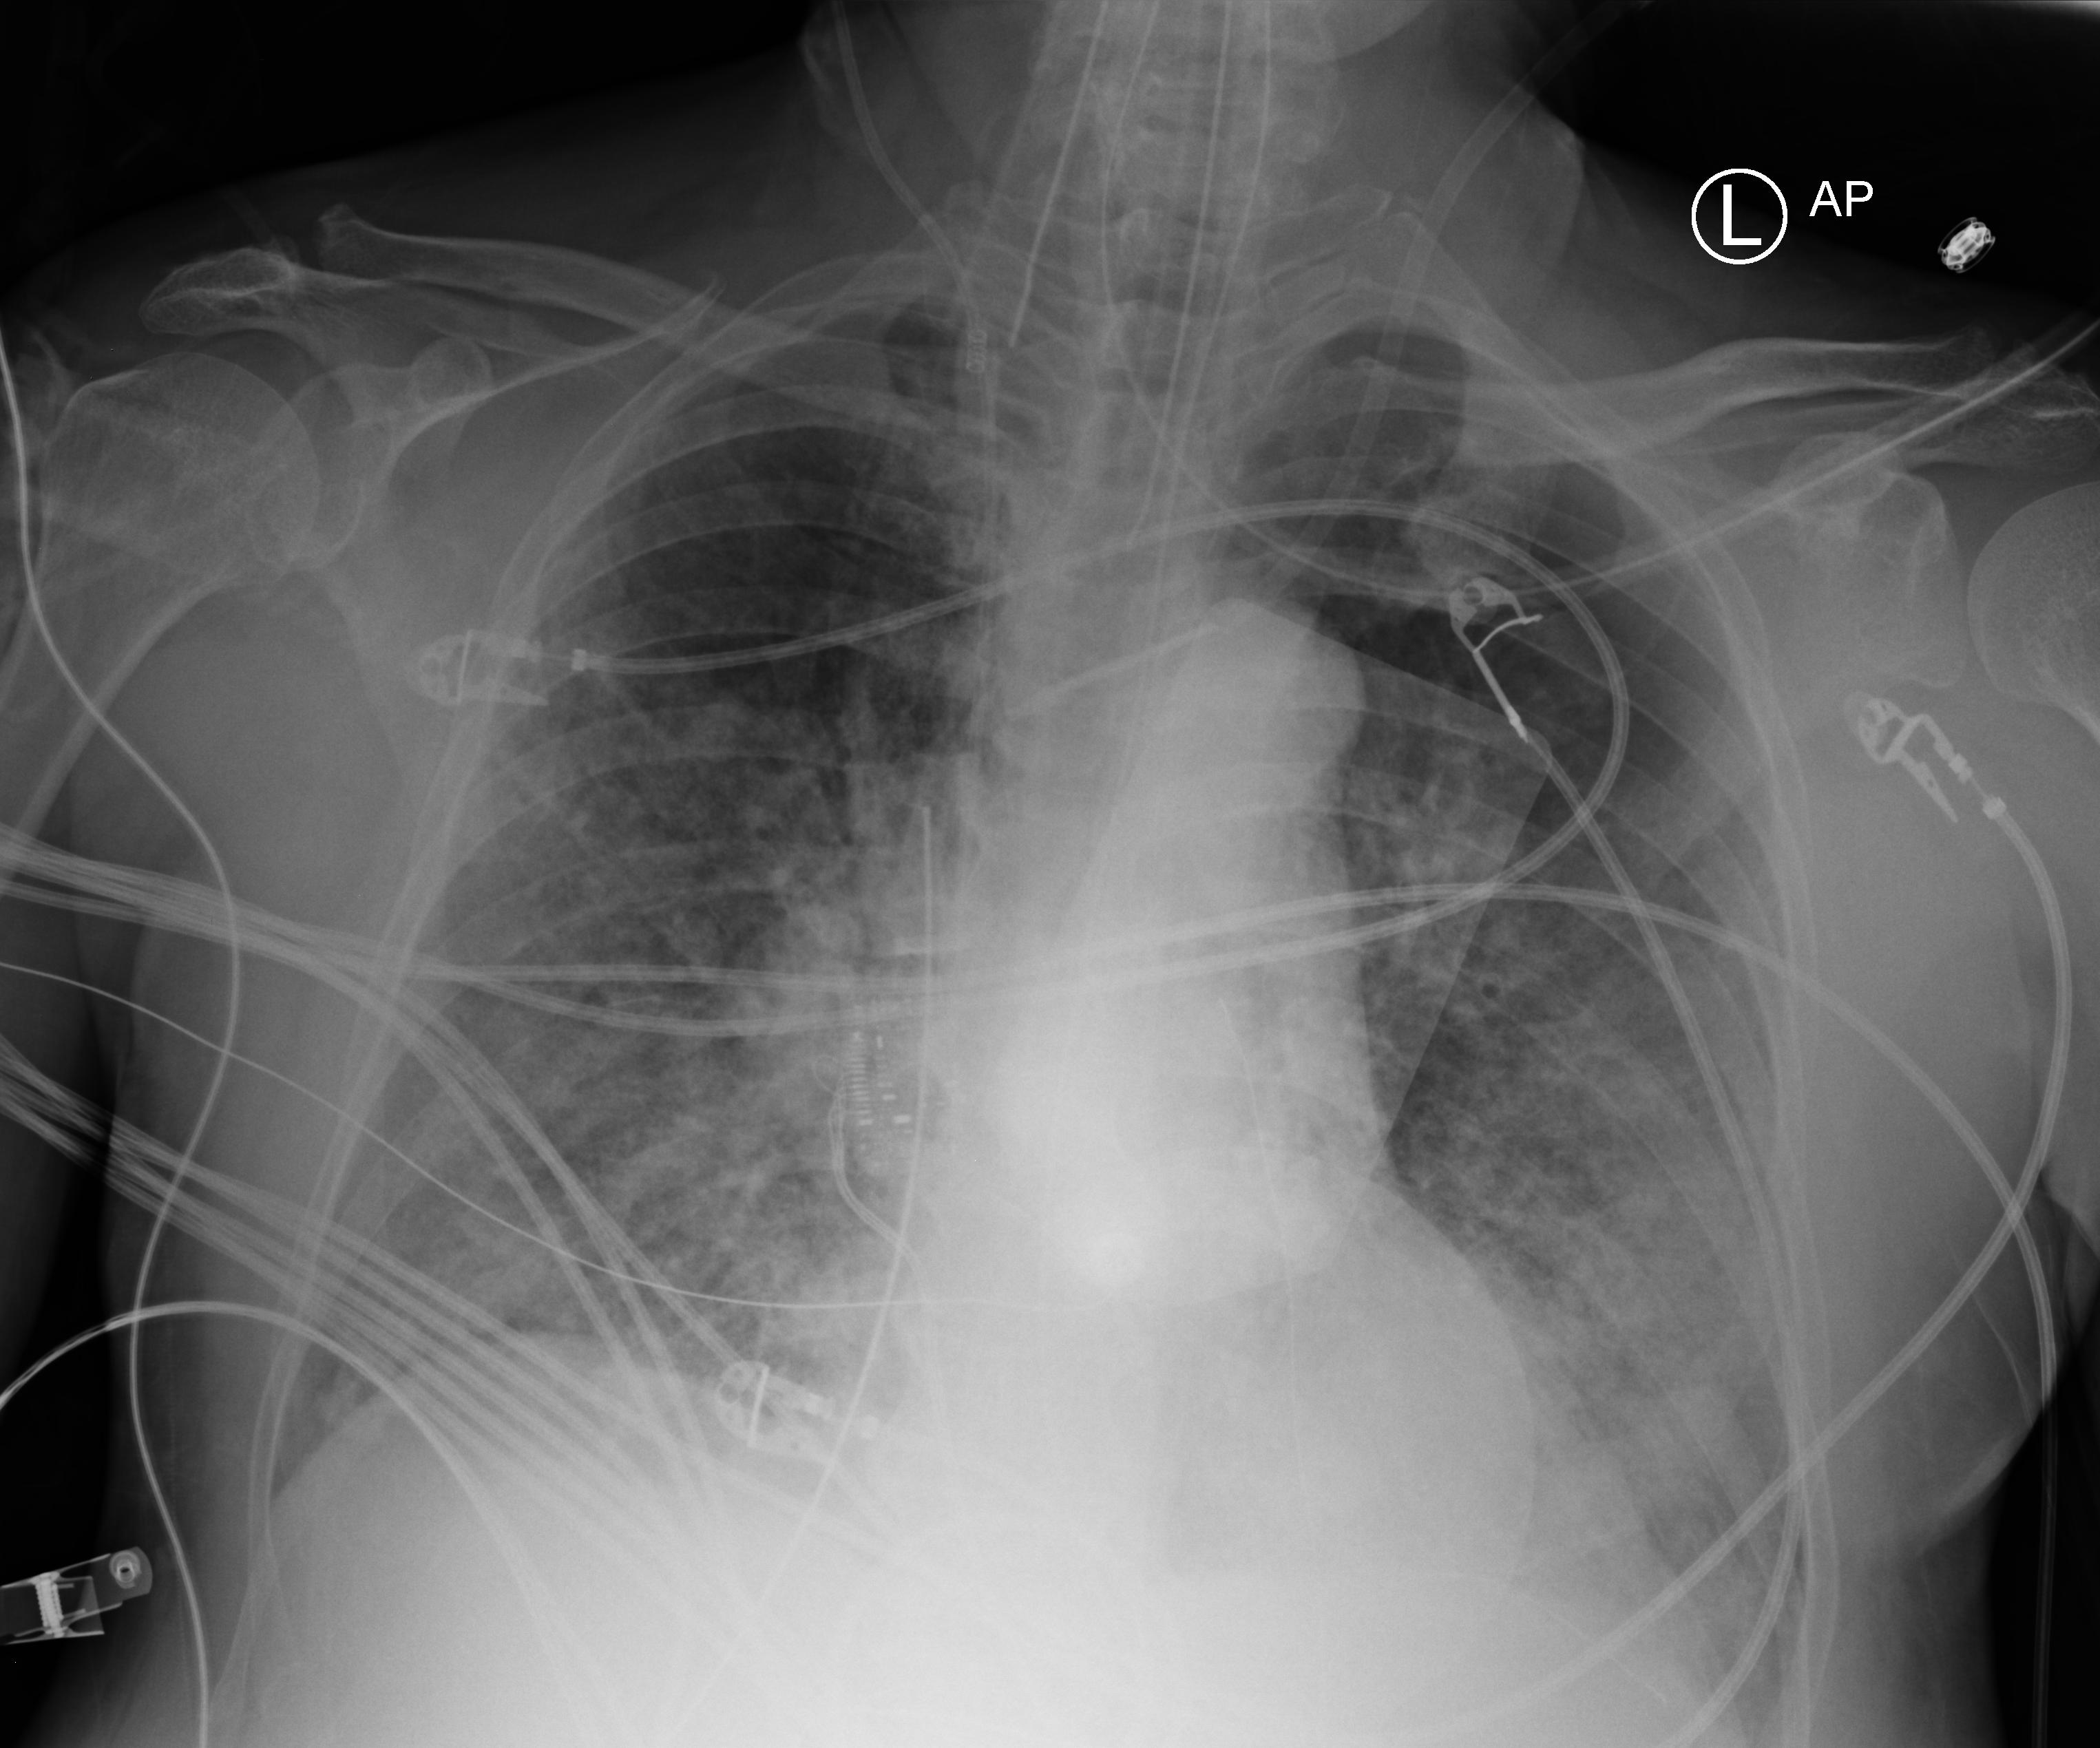
Bedside chest radiograph (computed radiography); anteroposterior (AP) projection. Male patient hospitalised with COVID-19, age 60–74 years.
From the hospital-stay record, not from the radiograph (when in the stay this image was taken is not recorded): mechanically ventilated during this hospital stay: yes; hypertension (admission record): yes; admitted to intensive care during this hospital stay: yes.